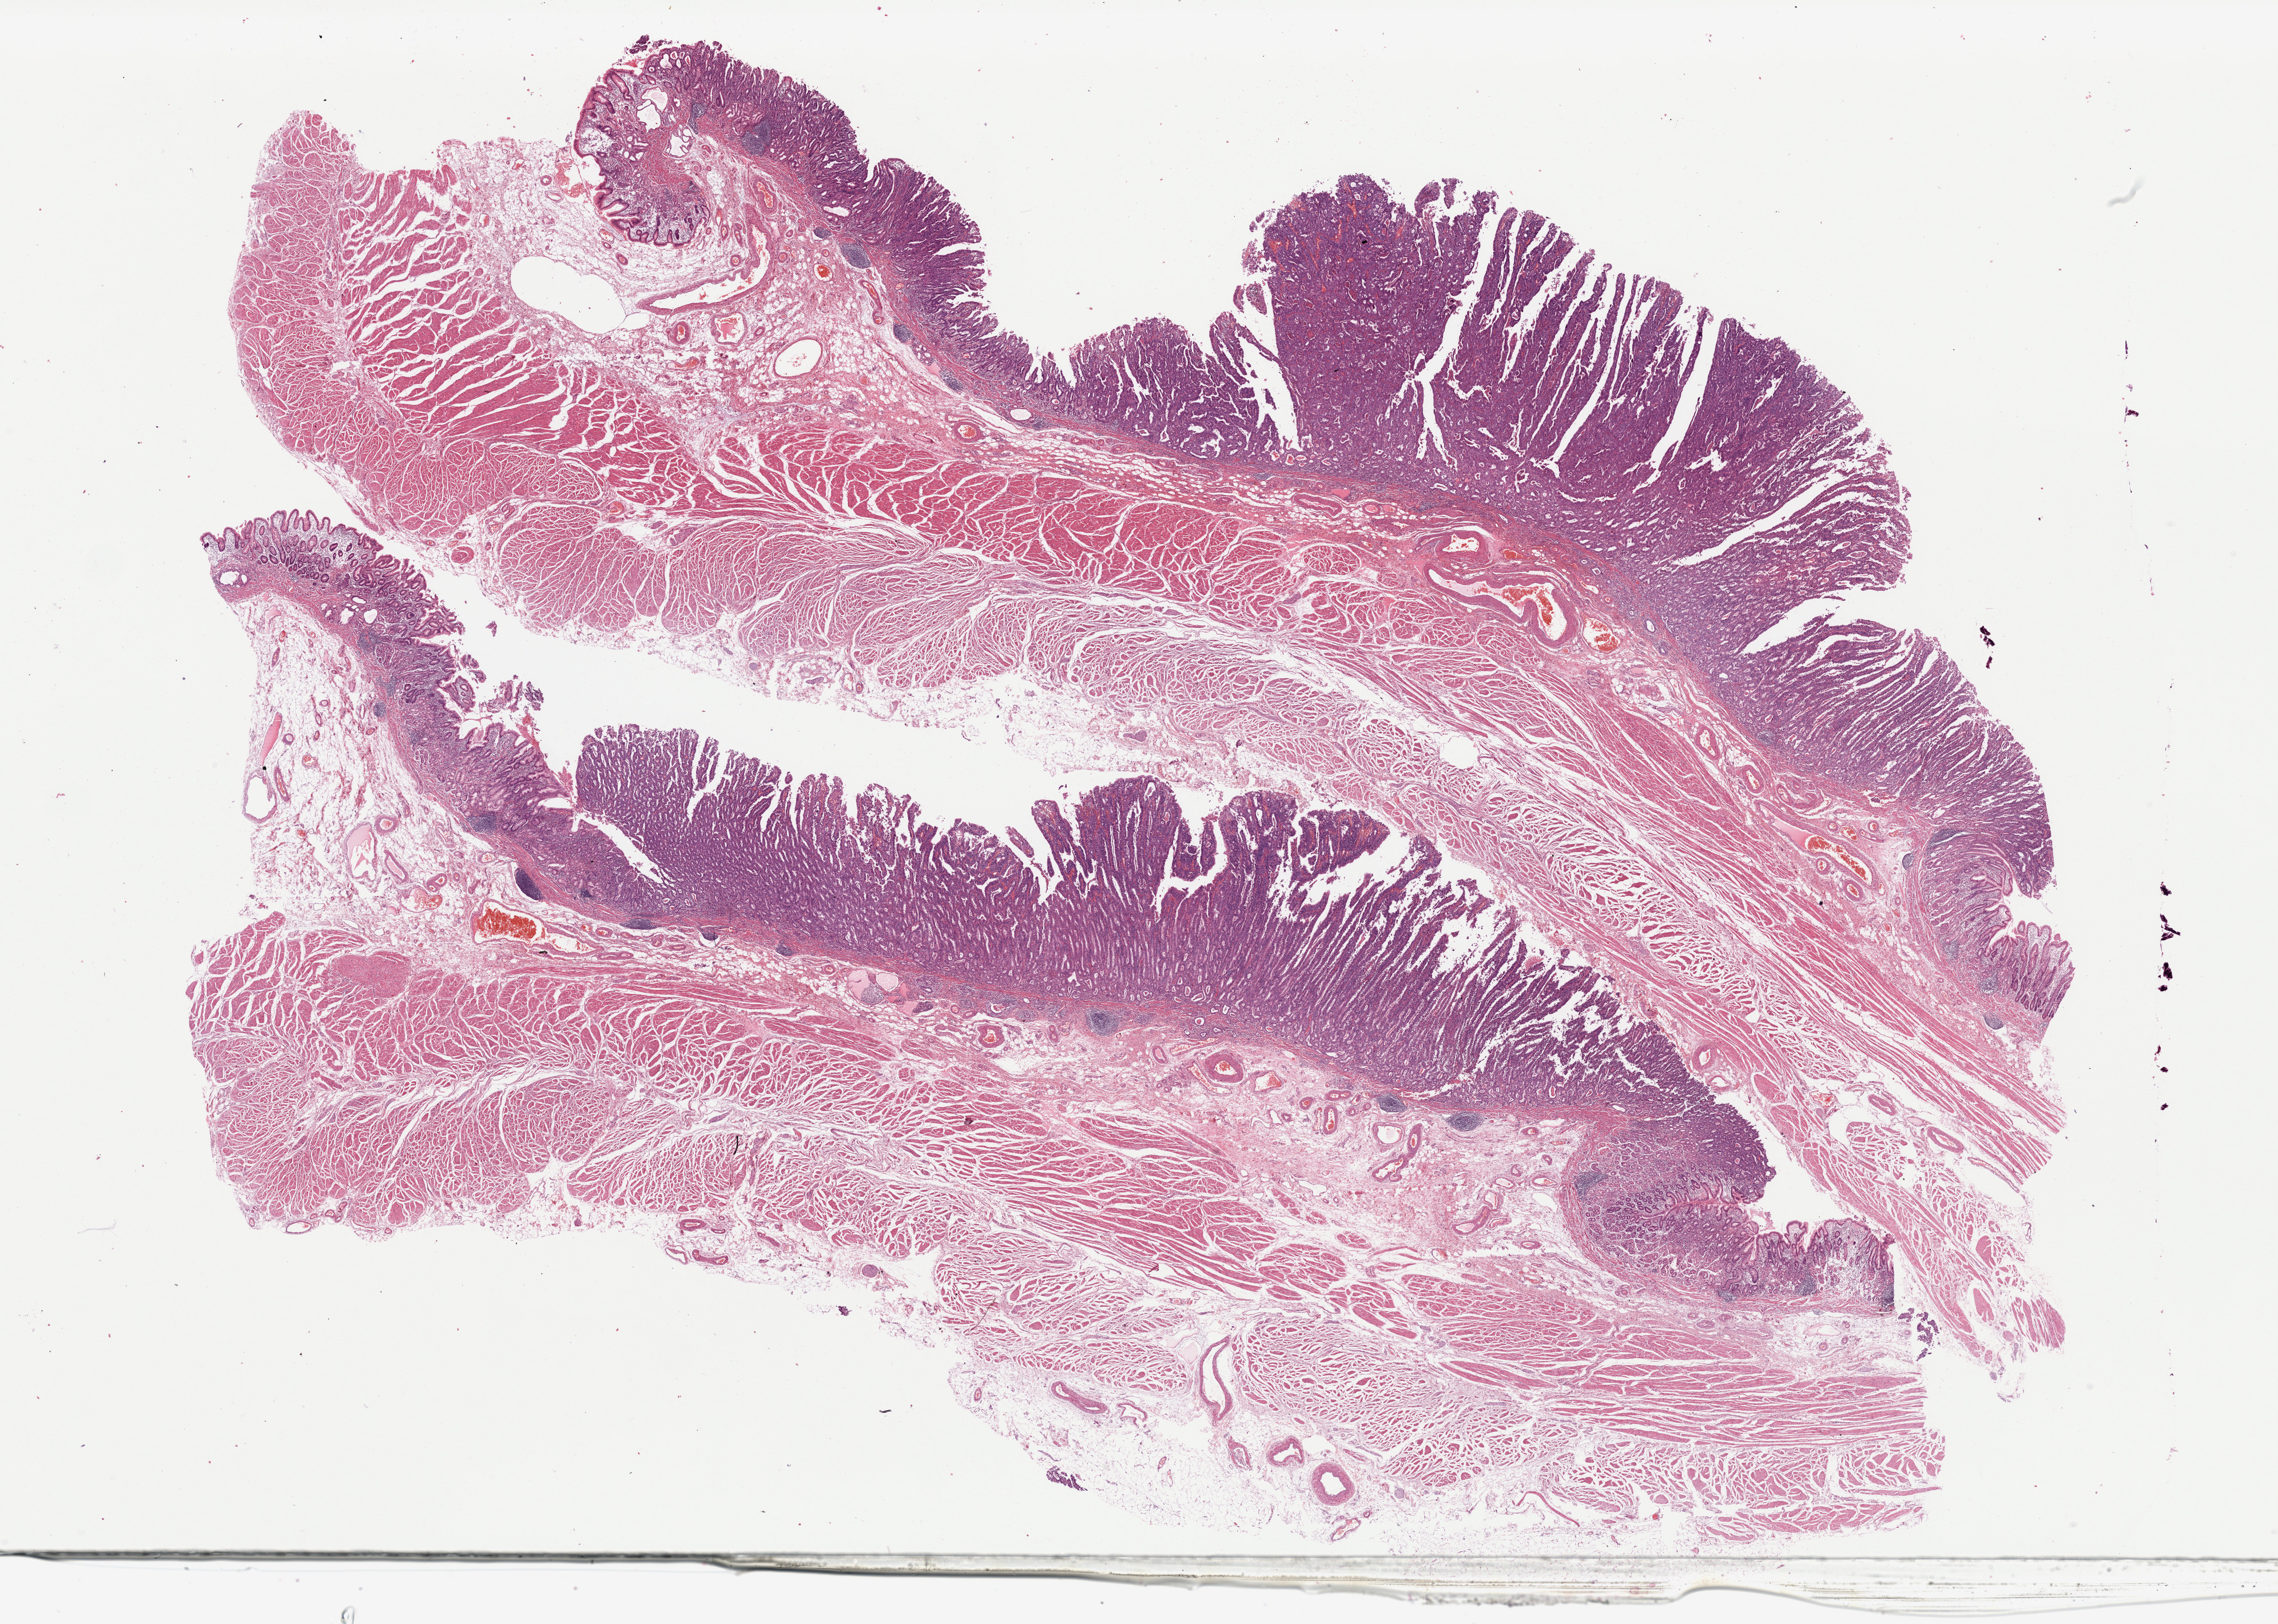
H&E whole-slide image, a low-resolution overview of the entire scanned area, about 31.5 x 22.5 mm (acquisition: 20x scan). Formalin-fixed paraffin-embedded (FFPE) diagnostic section. Stomach, primary tumour sample. Male, age 74 years at initial diagnosis. Histologic grade: G3 (poorly differentiated).
TNM: T1b N0 M0. AJCC pathologic stage: IA. Pathologic diagnosis: Papillary adenocarcinoma, NOS (cardia, NOS).